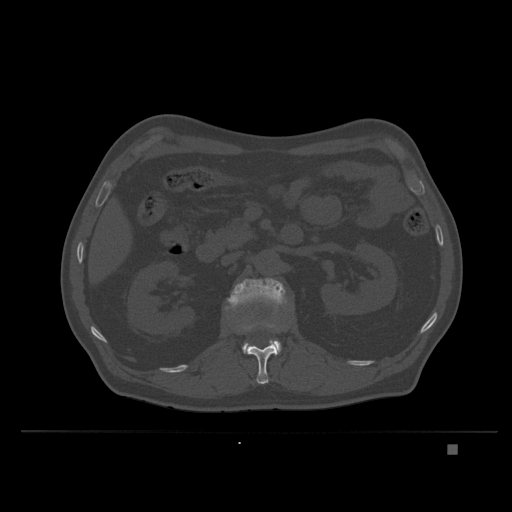
CT including the spine, one axial slice. Position 130 of 435 along the scan axis. Bone window (W 1800 / L 400 HU). 1.5 mm slice thickness. 512 × 512 image matrix. Male patient, age 73 years. From the clinical record (not read from this slice): primary cancer: skin.
Annotated regions visible in this slice (semi-automatic segmentation, software-assisted and operator-edited):
- L1 vertebra: box from (x=240, y=318) to (x=294, y=384) px
- L2 vertebra: (x=227, y=277)–(x=291, y=355)